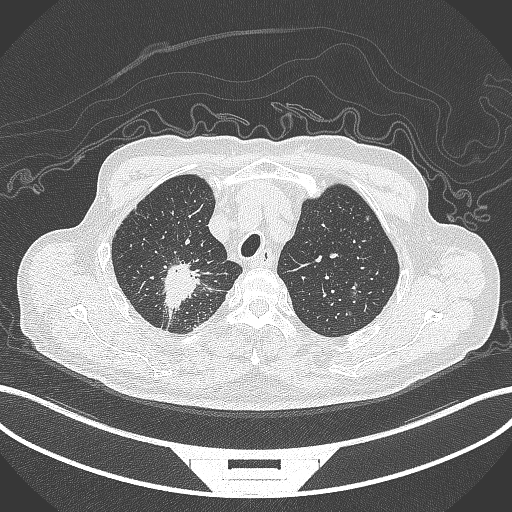
Chest CT, one axial slice; slice 312 of 407 in the series (ordered by position); reconstruction kernel B70f; 120 kVp; lung window (W 1500 / L -600 HU); 1 mm slice thickness; 512 × 512 image matrix, field of view 400 × 400 mm. Male patient, age 69 years. From the clinical record (not read from this slice): clinical TNM (as recorded): T1c N1 M1.
Outlined on this slice (bounding box drawn by a radiologist):
- lung tumour (recorded histology: adenocarcinoma): box from (x=156, y=260) to (x=208, y=319) px